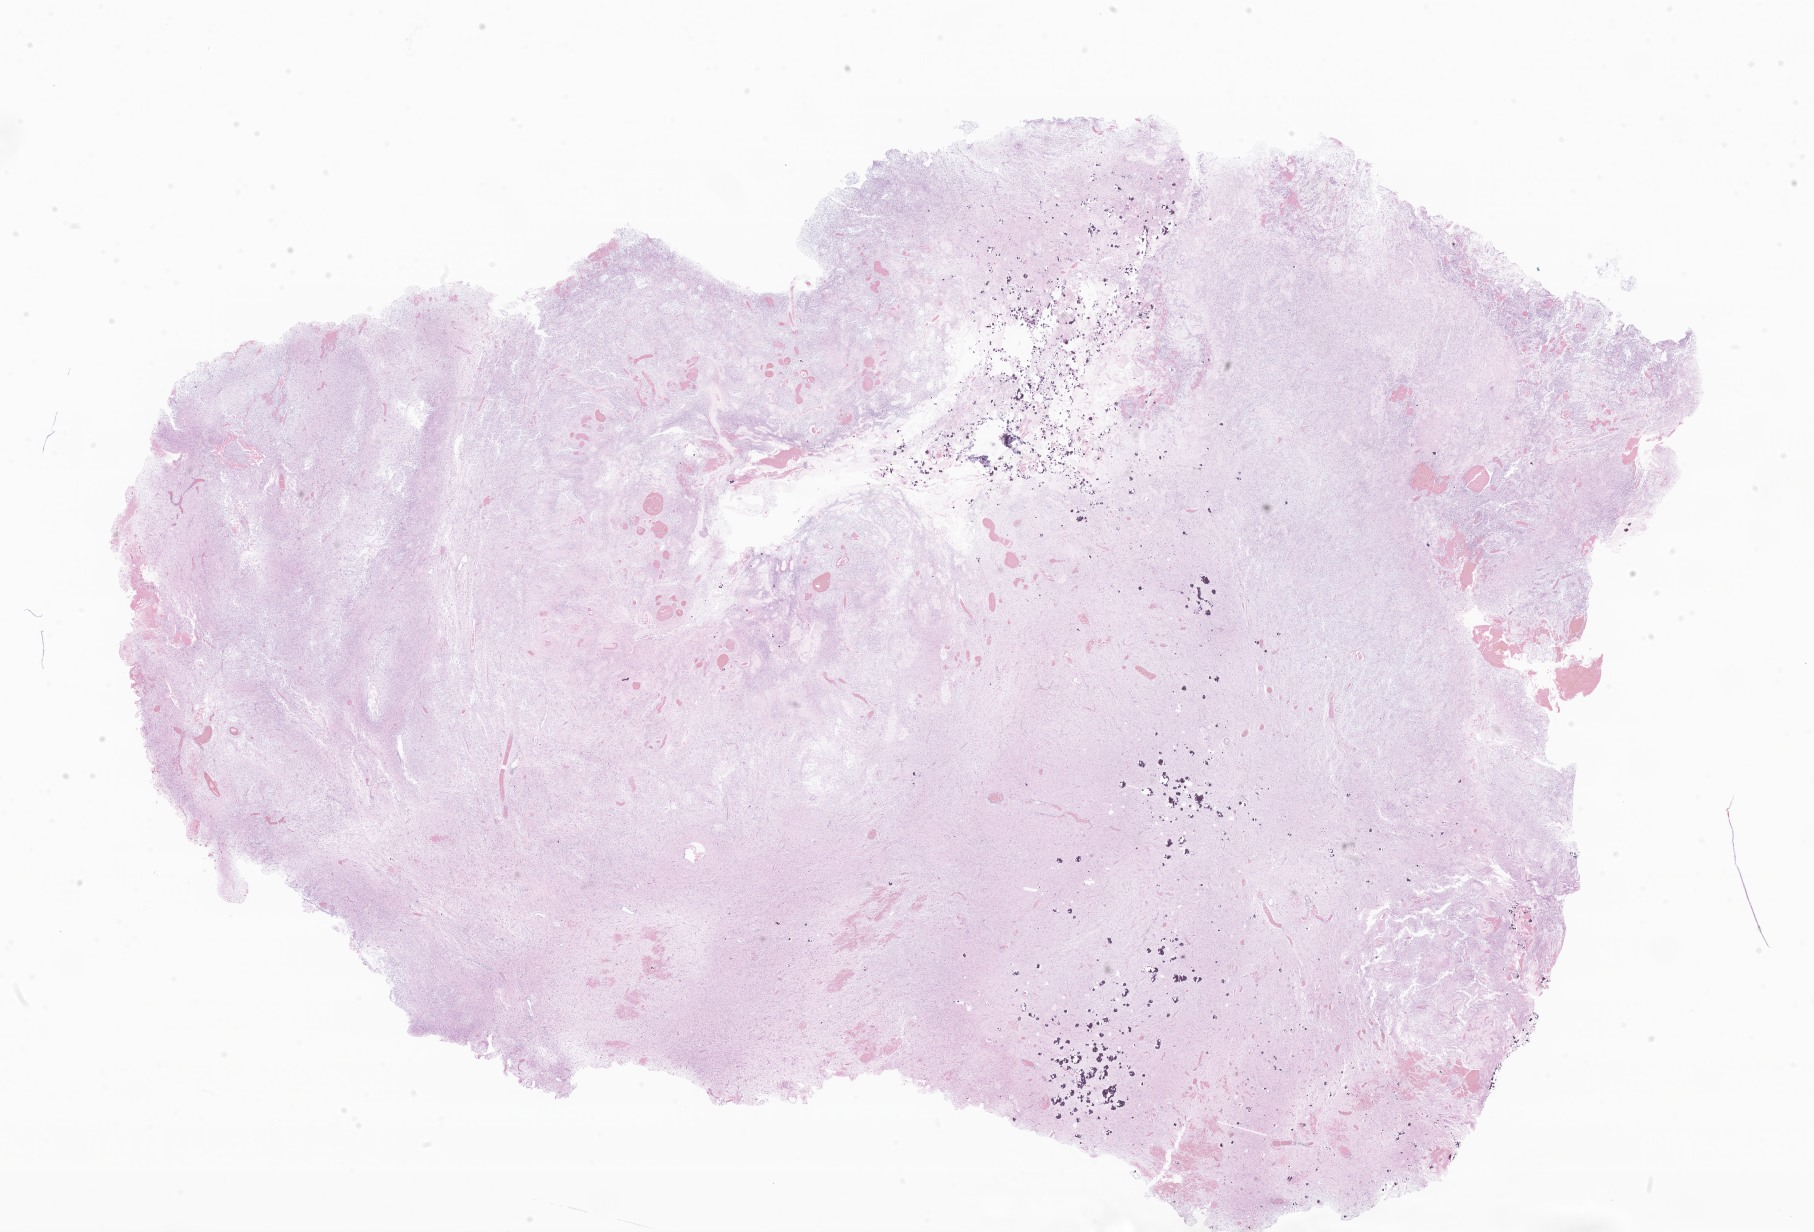
Digitized haematoxylin and eosin-stained section of tumor tissue from the brain — a low-resolution overview of the entire scanned area, about 30.6 x 20.8 mm, FFPE section. Patient female; age 187 months (15 years 7 months).
Recorded diagnosis: Glioma, malignant.